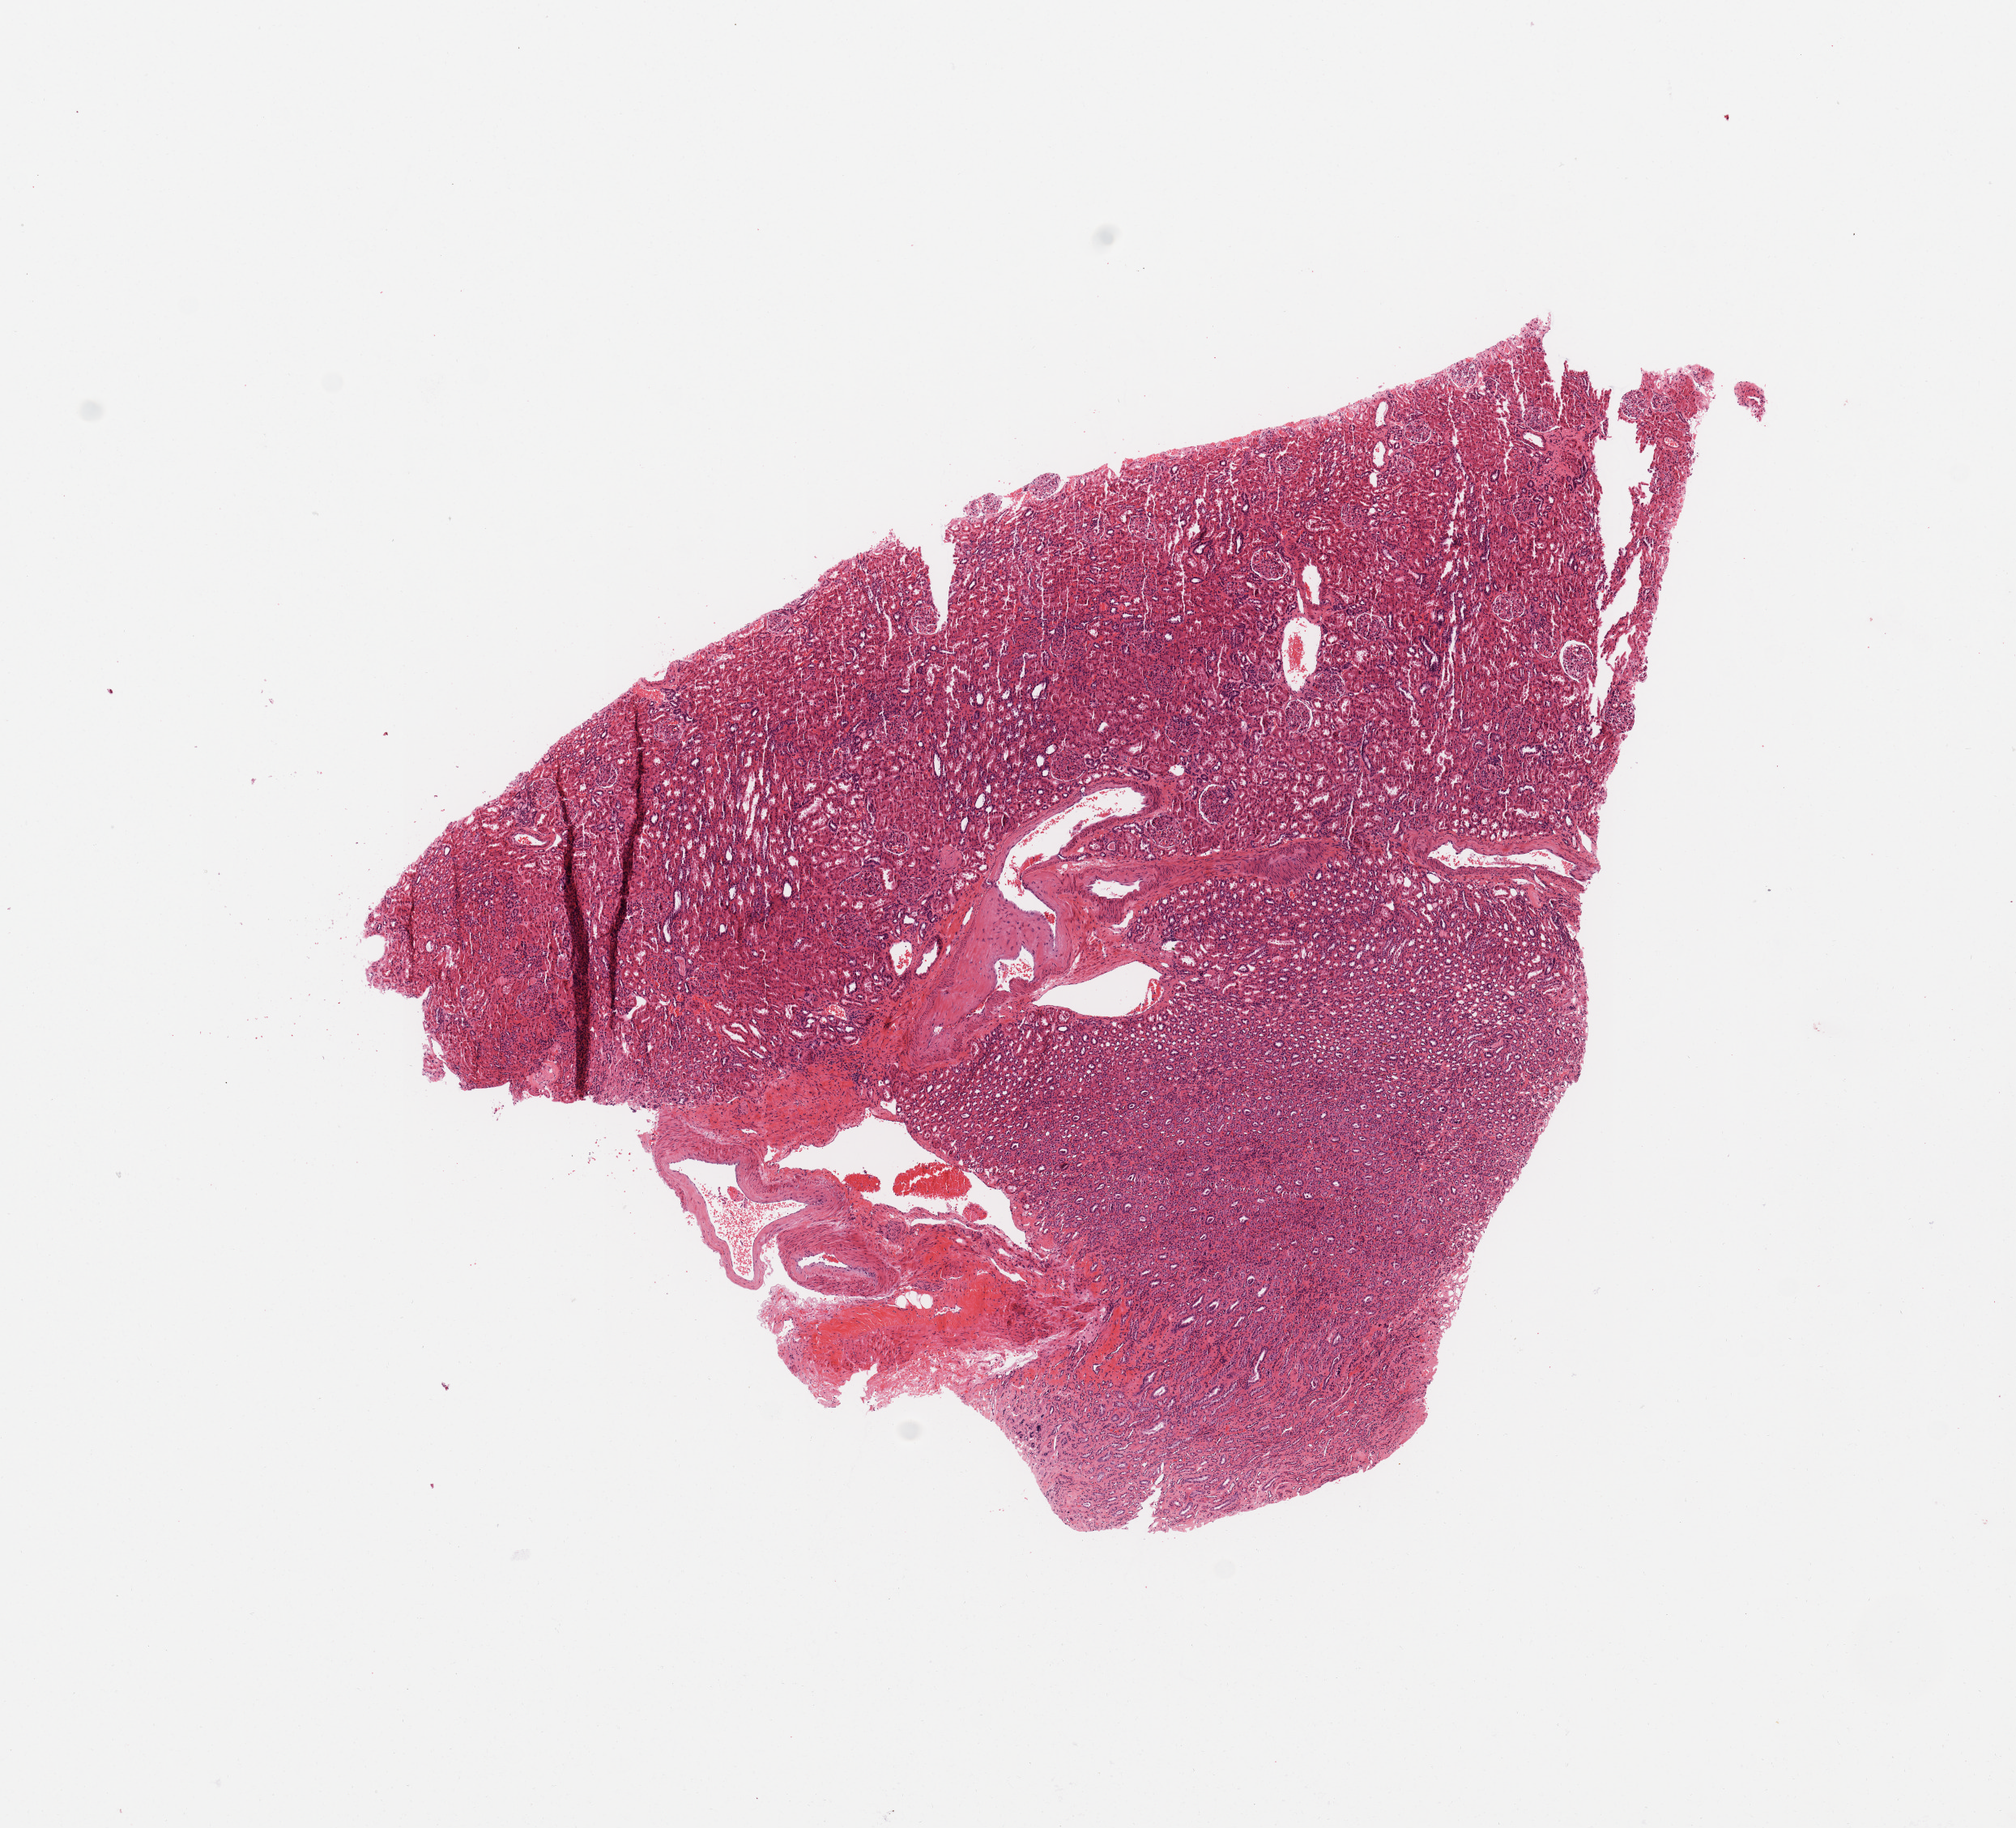
Whole-slide histology image, Hematoxylin and eosin (H&E) stained — a low-resolution overview of the entire scanned area, about 9.8 x 8.9 mm. Normal (non-tumour) tissue sample, sampled site: kidney. 52-year-old male patient.
• this section: normal (non-tumour) tissue from the same patient
• patient diagnosis: Renal cell carcinoma, NOS